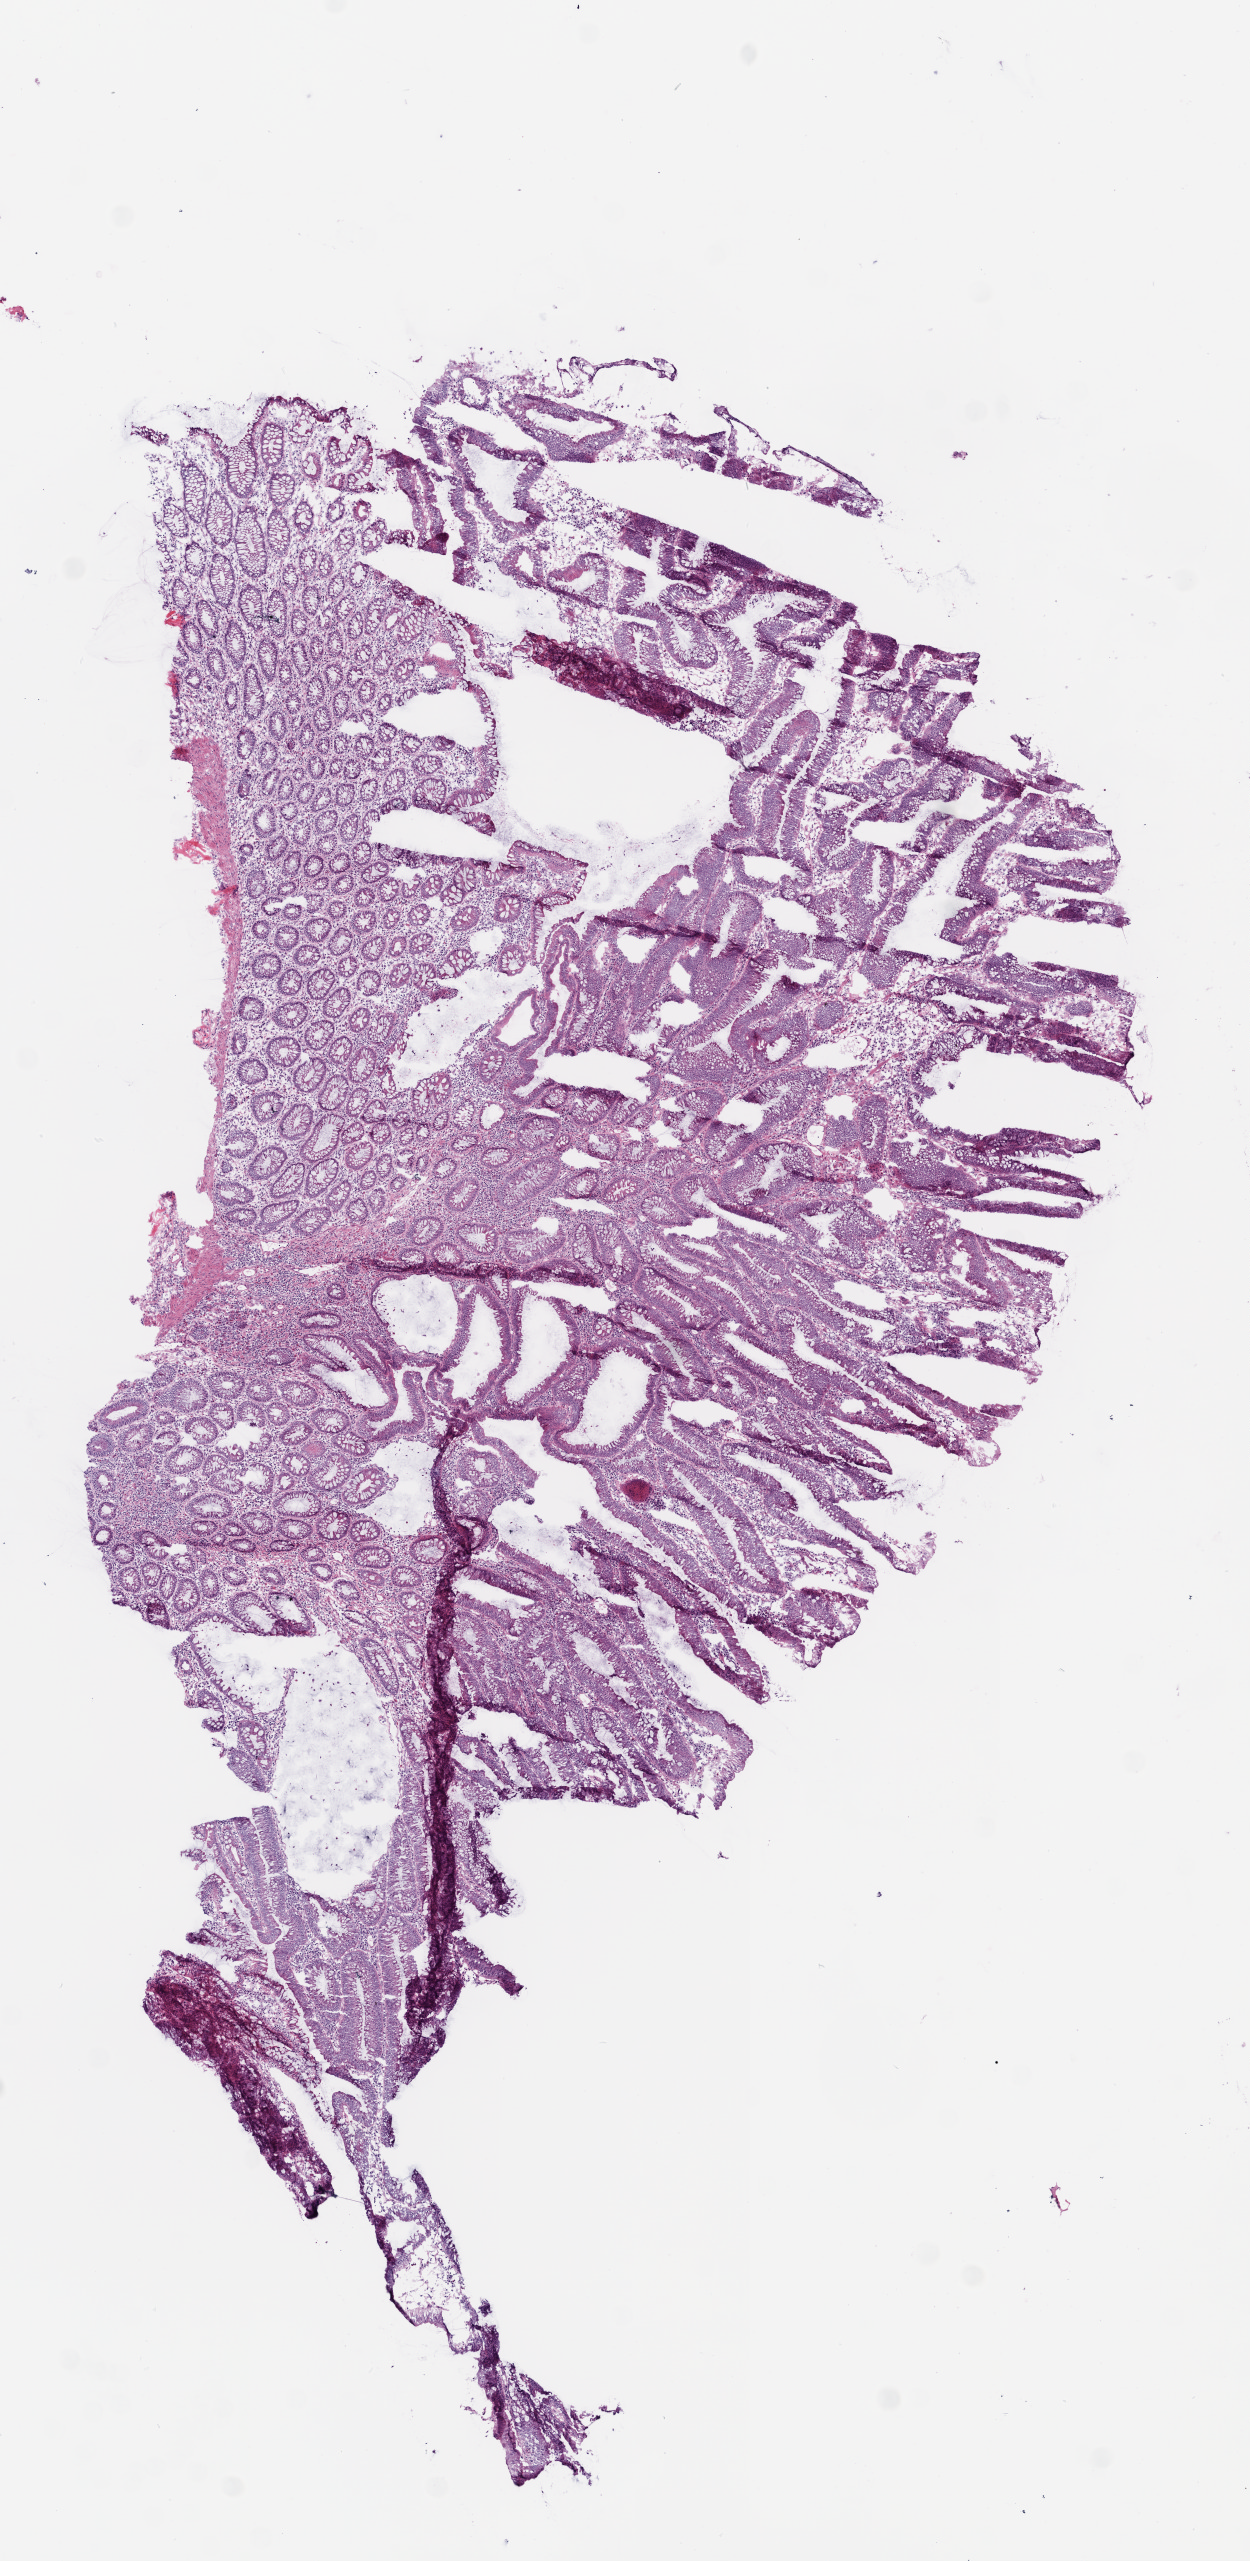
H&E whole-slide image, low-resolution overview of the scanned area, about 5.0 x 10.3 mm. Frozen section from the bottom of the tissue portion. Primary tumour sample from the colon. Male, age 67 years at initial diagnosis. Slide review estimates, as recorded: tumour cells 60%, tumour nuclei 60%, normal cells 30%, stromal cells 10%, necrosis 0%.
AJCC pathologic stage: IIA. Pathologic diagnosis: Adenocarcinoma, NOS (ascending colon). Lymph nodes positive (case pathology): 0 of 18 examined.